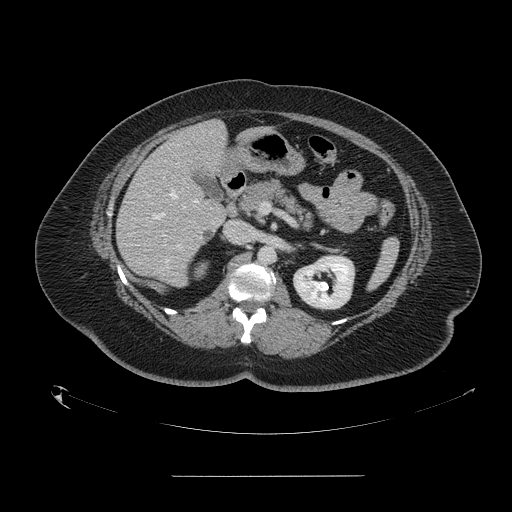
Contrast-enhanced abdominal CT, one axial slice. Position 78 of 164 along the scan axis. Intravenous contrast given. Soft-tissue window (W 400 / L 40 HU). 2.5 mm slice thickness. 512 × 512 image matrix. Female patient, age 52 years. Case-level facts recorded for this patient, not image findings: diagnosis: colorectal cancer liver metastases, imaged before liver resection; multiple liver metastases: yes; largest metastasis: 3.5 cm; disease in both lobes: no.
Annotated regions visible in this slice (manually delineated by an expert):
- hepatic veins: bounding box <153,191,185,219> (left, top, right, bottom; pixels)
- liver: <117,121,227,286>
- planned liver remnant (the part of the liver to remain after resection): <177,121,226,171>
- portal vein (with intrahepatic branches): <162,177,198,237>
- liver metastasis: <203,230,213,239>